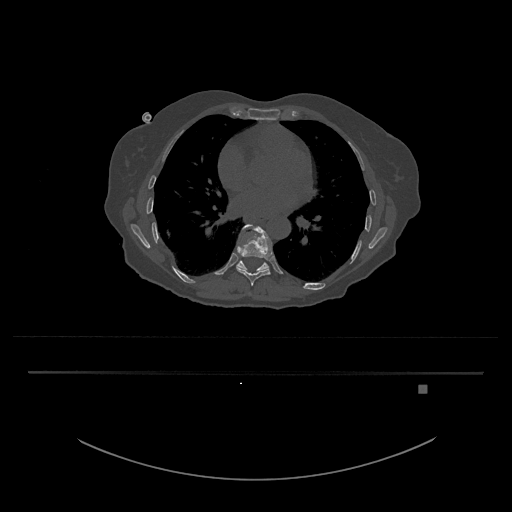
CT including the spine, one axial slice; slice 746 of 797 in the series (ordered by position); reconstruction kernel Br40s/3; bone window (W 1800 / L 400 HU); 0.5 mm slice thickness; 512 × 512 image matrix, field of view 500 × 500 mm. Female patient, age 57 years. Case-level facts recorded for this patient, not image findings: primary cancer: cervical.
Structures marked on this image (semi-automatic segmentation, software-assisted and operator-edited):
- T10 vertebra: bounding box <236,257,269,273> (left, top, right, bottom; pixels)
- T9 vertebra: <237,225,273,286>